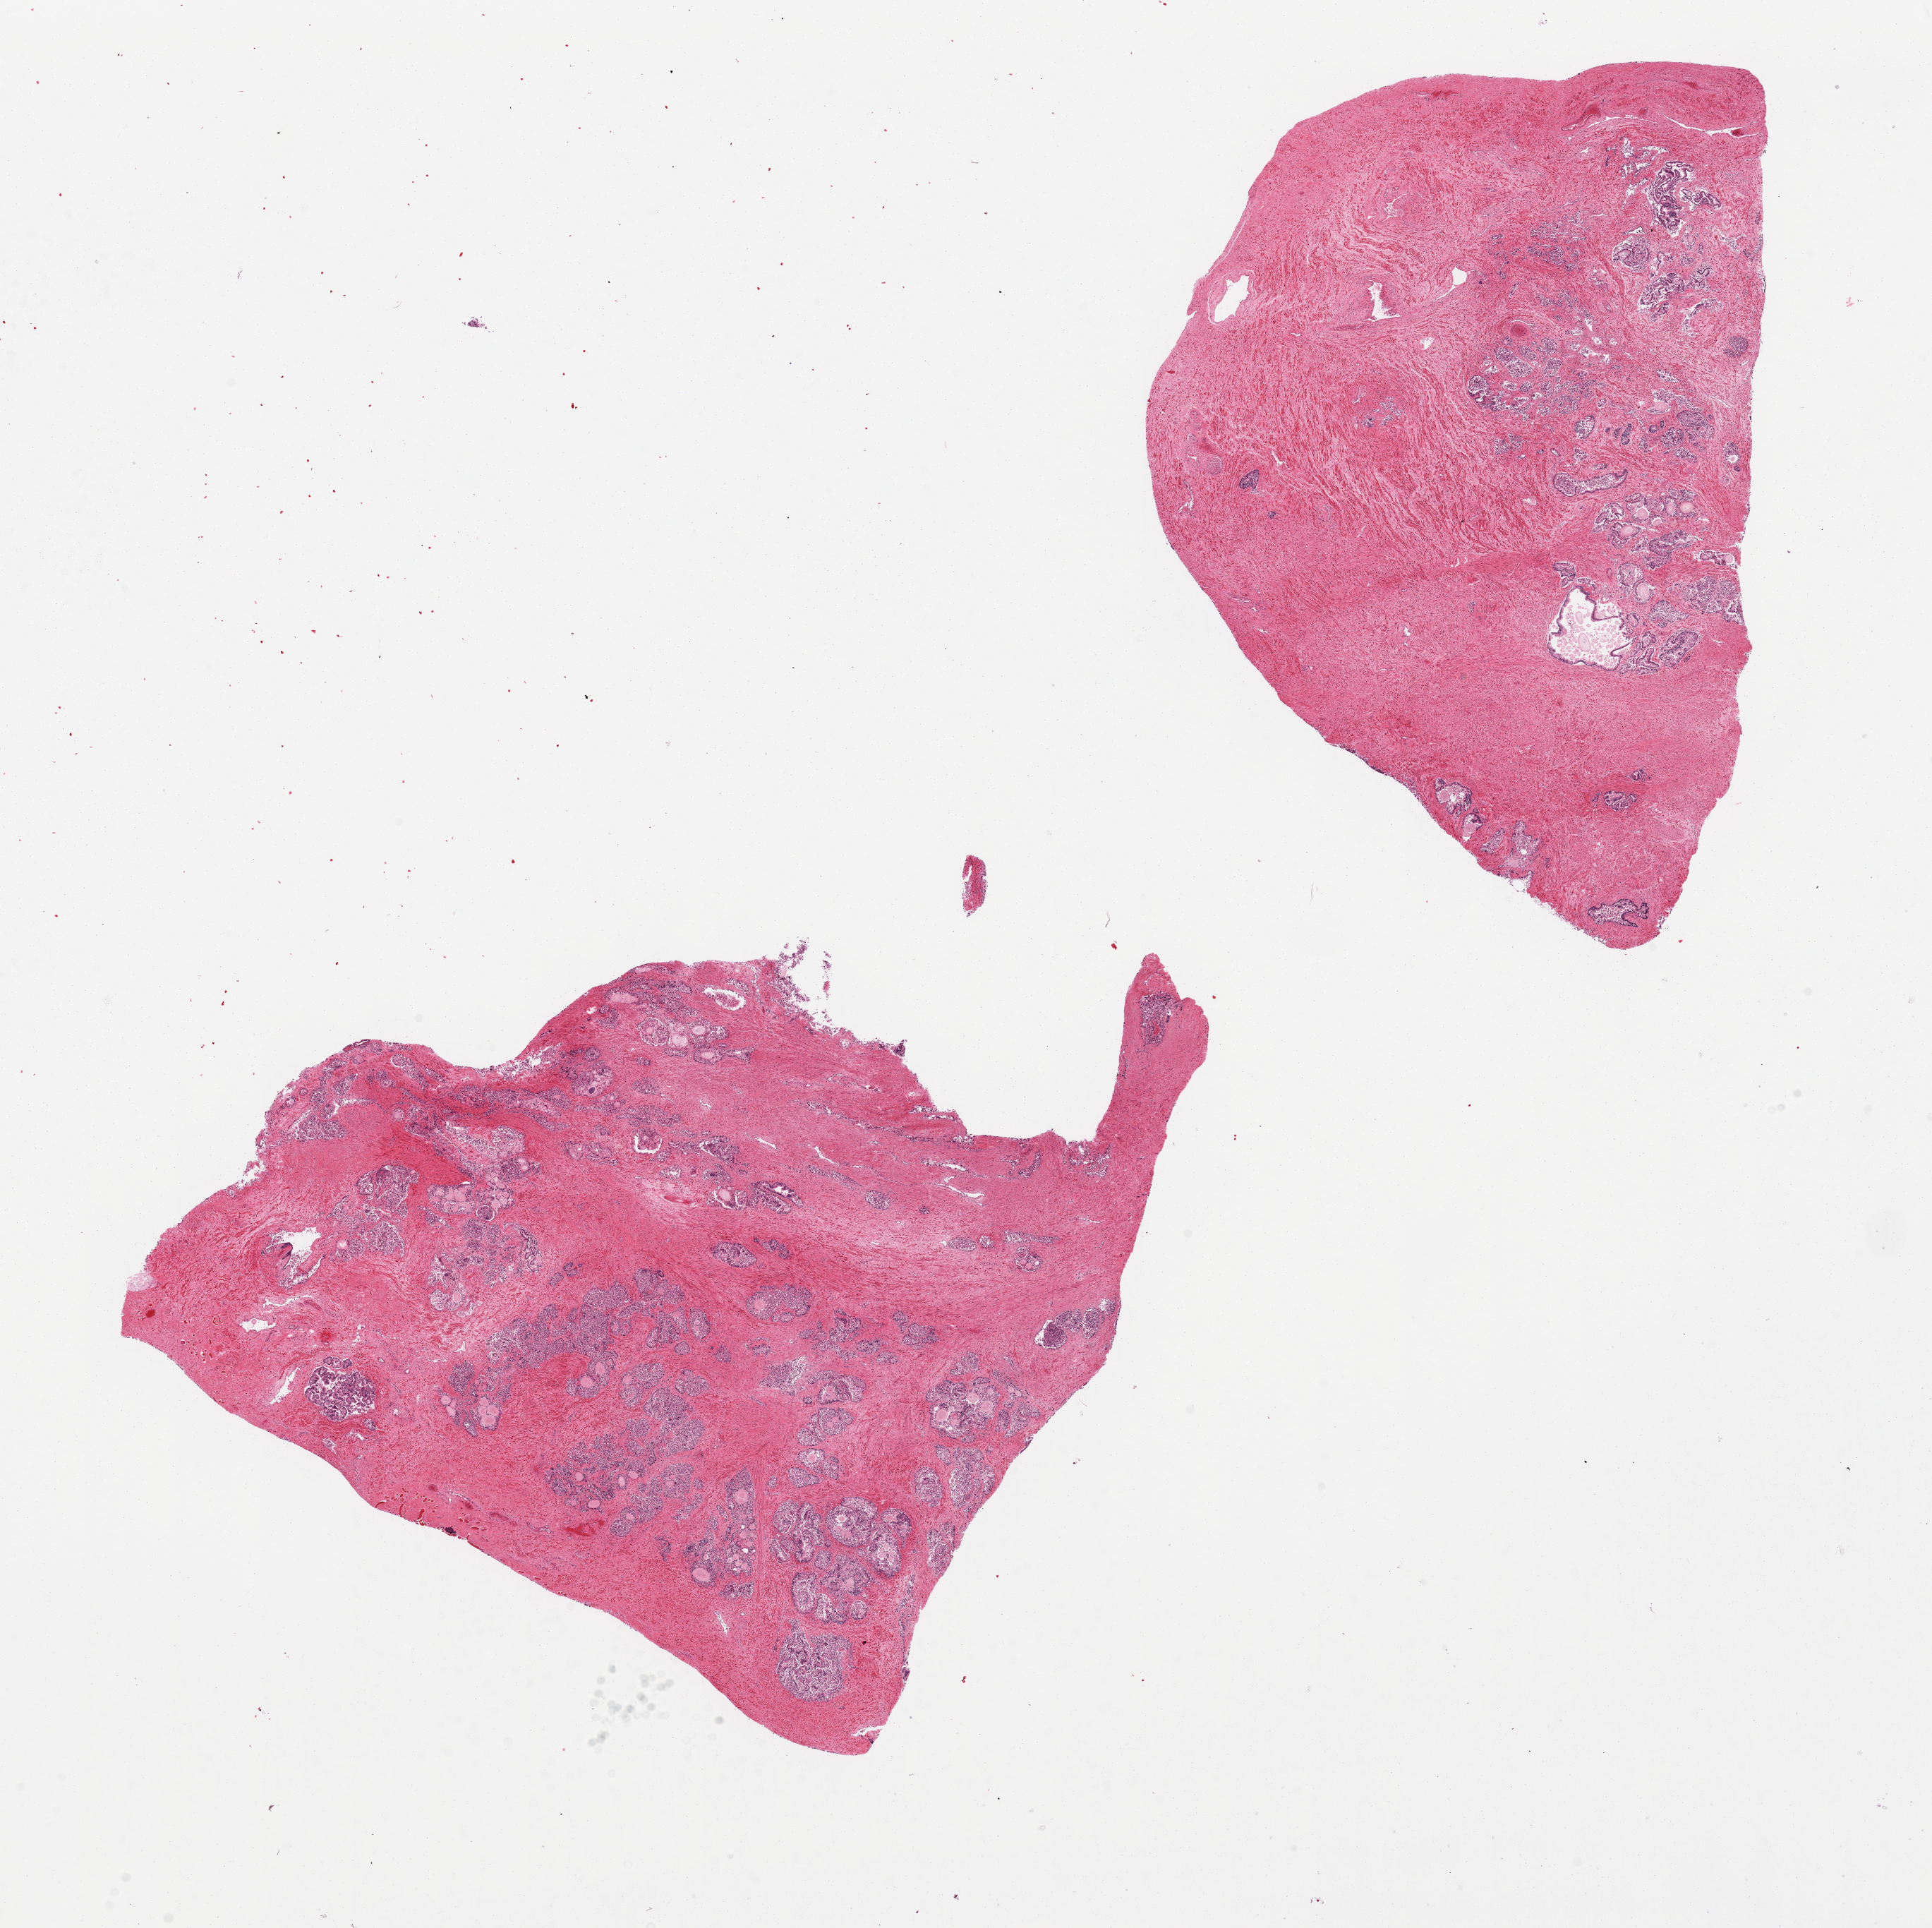
Digitized H&E-stained section, a low-resolution overview of the entire scanned area, about 21.7 x 21.6 mm (from a 20x scan), PAXgene-fixed paraffin-embedded (PFPE) section, section of prostate (target tissue), donor tissue sample.
Pathologist's review note for this sample: 2 pieces: glands=3; stroma=2.